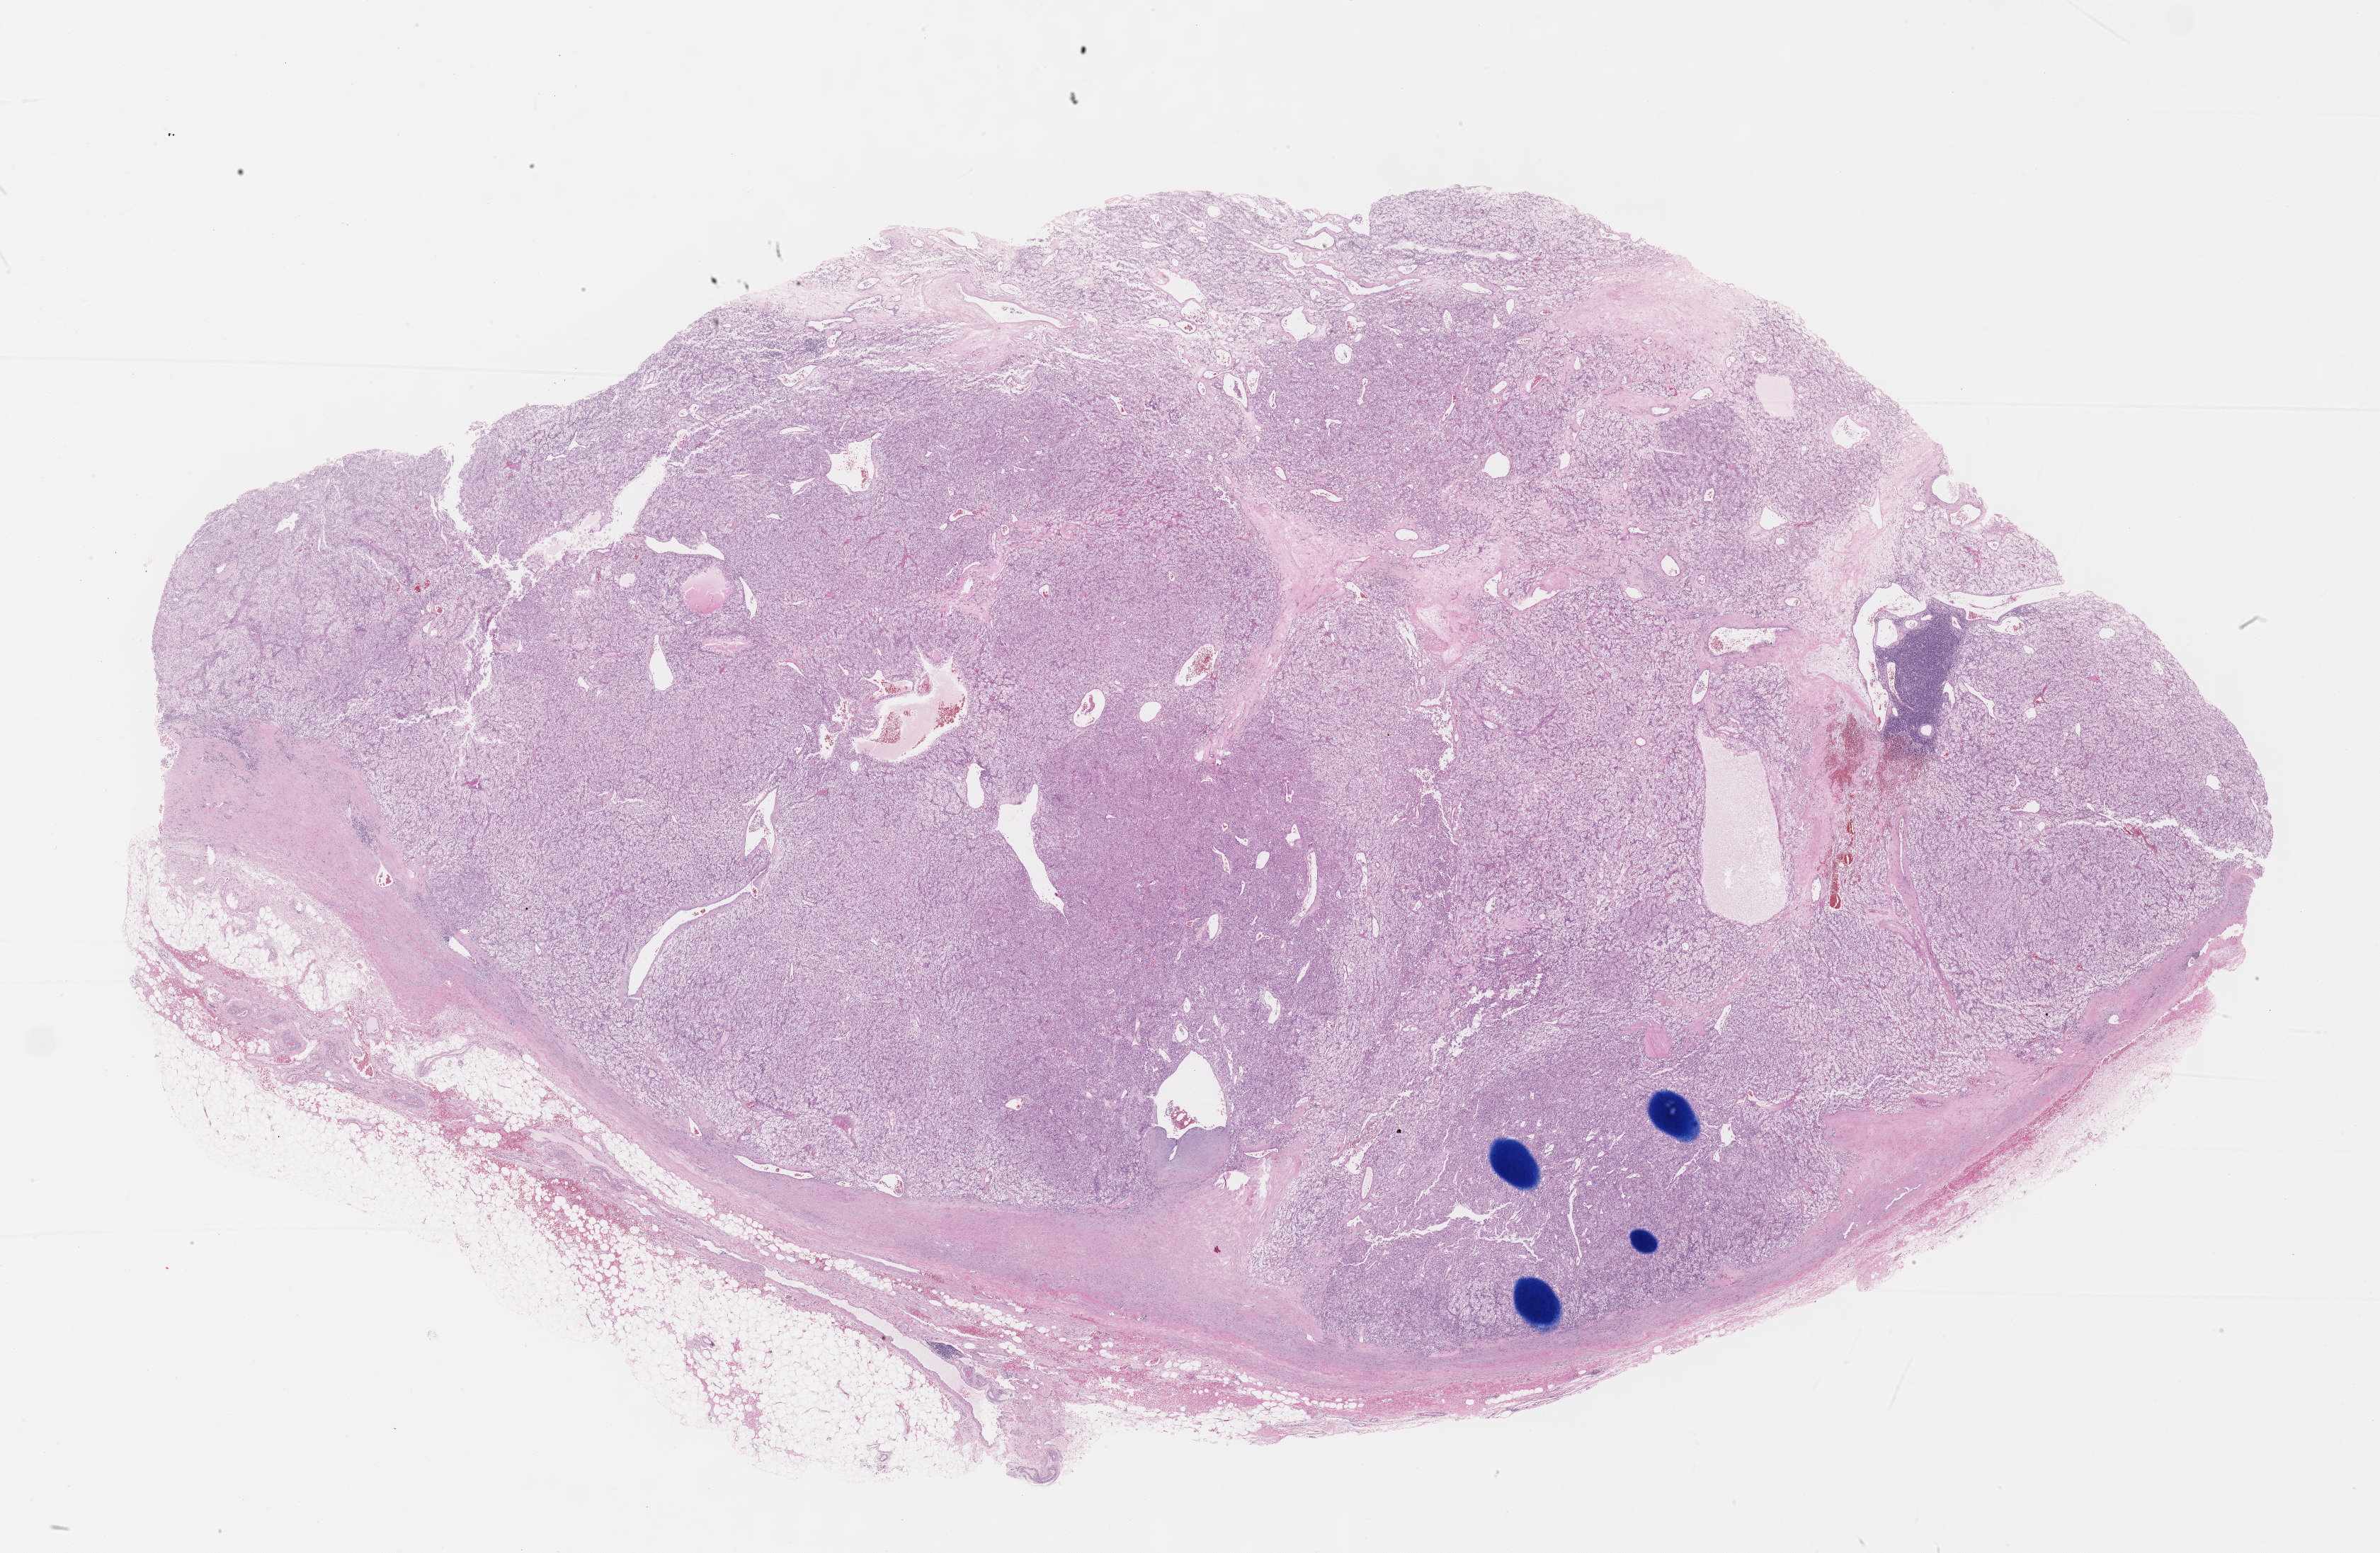
H&E whole-slide image — whole scanned area (about 27.2 x 17.7 mm) shown as a low-resolution overview; formalin-fixed paraffin-embedded (FFPE) diagnostic section; primary tumour sample from the kidney. Female, age 72 years at initial diagnosis. Histologic grade: G3 (poorly differentiated).
- TNM: T3a NX M0
- pathologic diagnosis: Clear cell adenocarcinoma, NOS
- AJCC pathologic stage: III